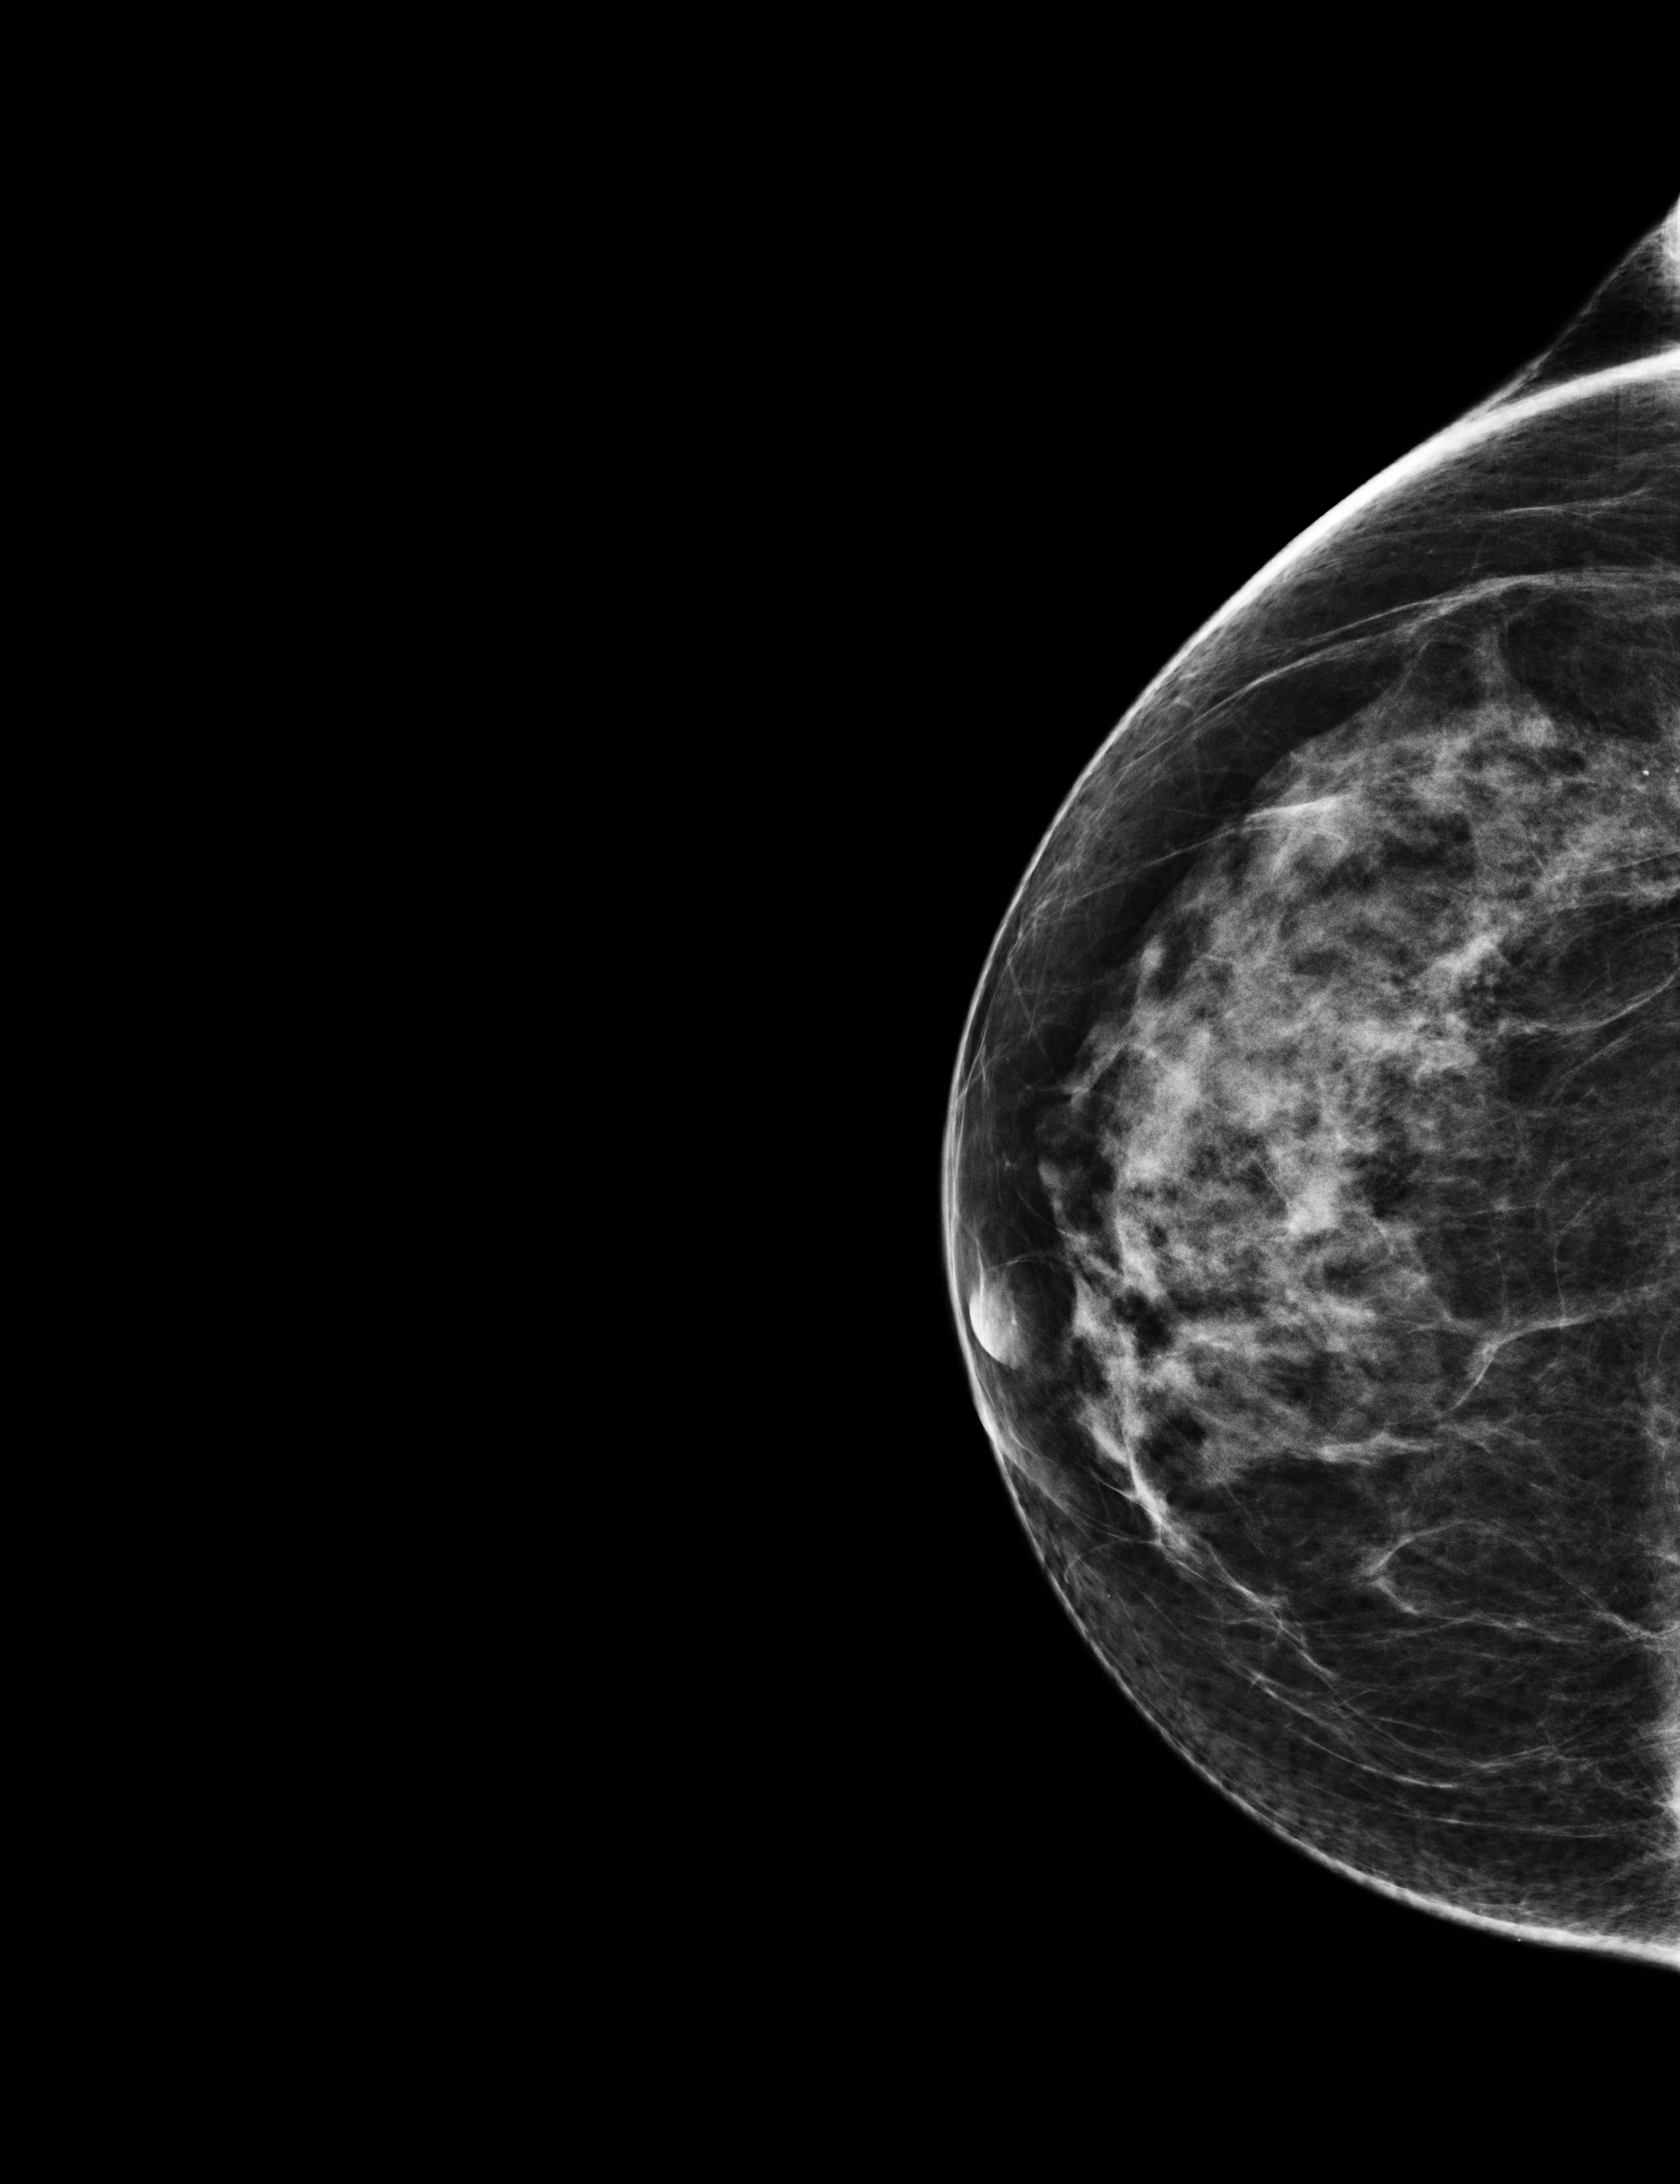
Digital mammogram (FFDM); right breast; CC view; screening examination; compressed breast thickness 61 mm. Patient aged 66 years (female).
Final BI-RADS category for the screening round (tomosynthesis exam, both breasts): category 1.